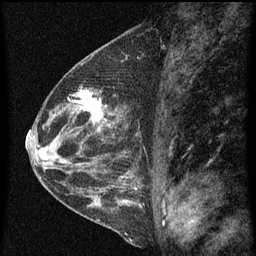
Breast MRI (dynamic contrast-enhanced), one sagittal slice; position 27 of 60 along the scan axis; dynamic contrast-enhanced series, image 2 of 4 at this slice position (ordered by acquisition); 1.5 T; TE 4.2 ms, TR 8 ms; 2 mm slice thickness; 256 × 256 image matrix, field of view 180 × 180 mm. Female patient, age 48 years.
Outlined on this slice (semi-automatic segmentation, software-assisted and operator-edited):
- analysis volume of interest (the breast-tissue region the enhancement analysis was run in; not a lesion): bounding box [x1, y1, x2, y2] px = [73, 86, 115, 139]
- tumour enhancement mask (voxels above the 70 % enhancement threshold inside the analysis volume of interest): [78, 90, 114, 133]